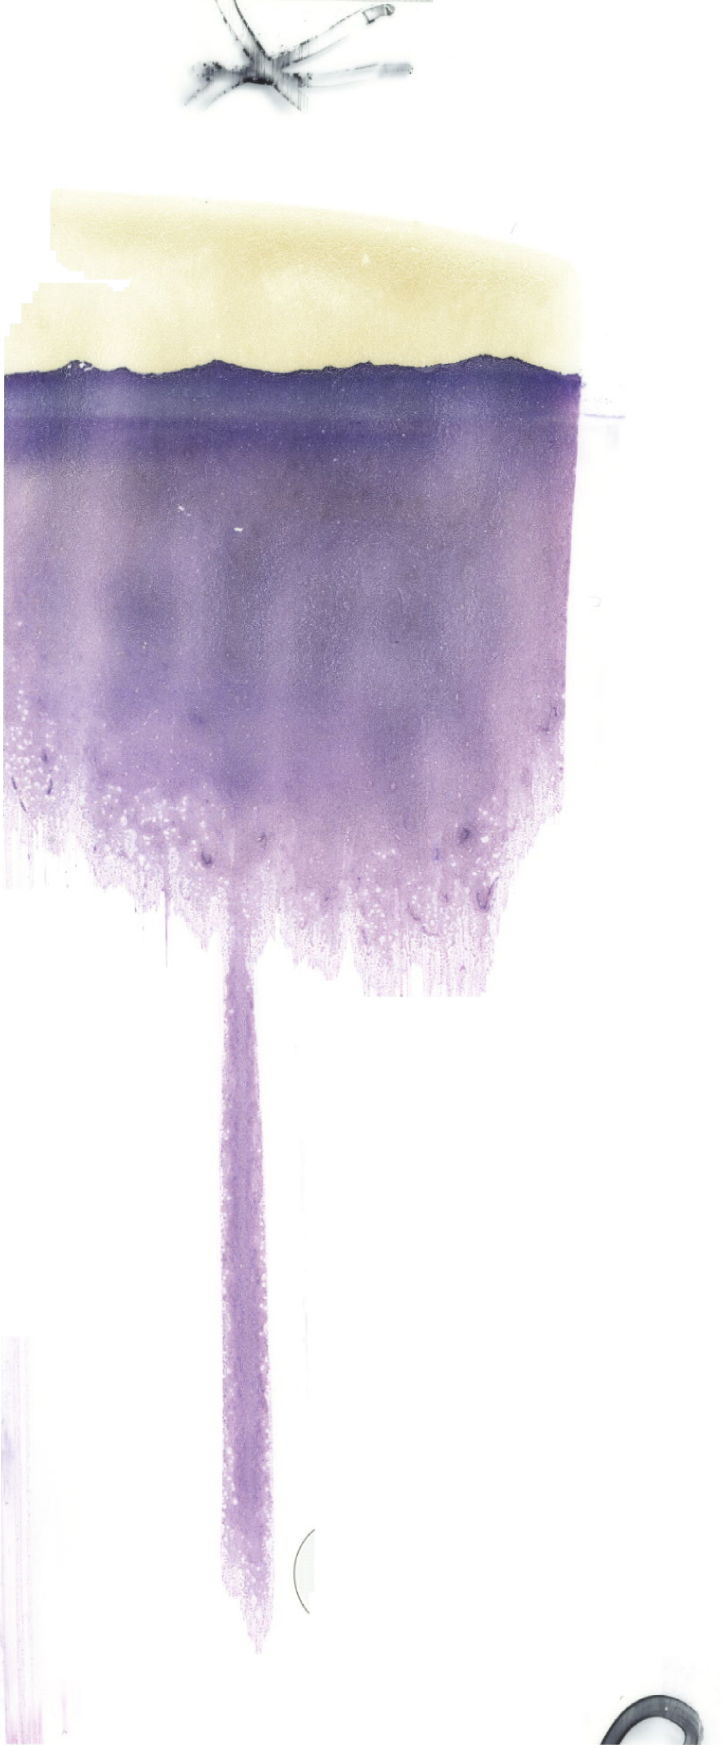
Bone marrow aspirate smear, May-Grünwald–Giemsa stain, whole-slide image, whole scanned area (about 20.5 x 49.5 mm) shown as a low-resolution overview. Patient sex: female.
- diagnosis: Acute Megakaryoblastic Leukemia